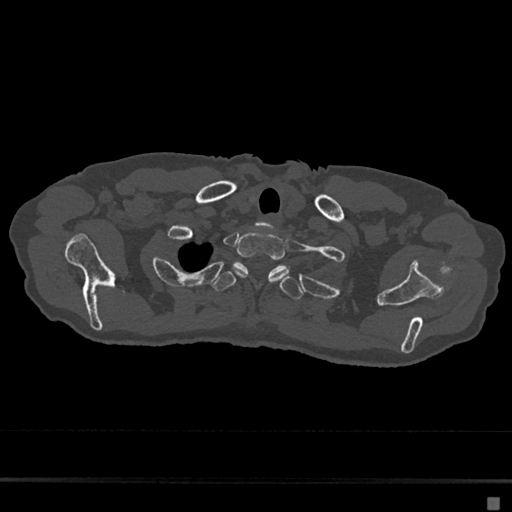
CT including the spine, one axial slice; position 595 of 797 along the scan axis; reconstruction kernel Br40s/3; 120 kVp; bone window (W 1800 / L 400 HU); 0.5 mm slice thickness; 512 × 512 image matrix, field of view 360 × 360 mm. Patient: female, 68 years. From the clinical record (not read from this slice): primary cancer: renal.
Structures marked on this image (semi-automatically segmented with operator editing):
- T1 vertebra: bounding box (x1, y1, x2, y2) in pixels: (233, 232, 290, 281)
- T2 vertebra: (211, 262, 304, 300)